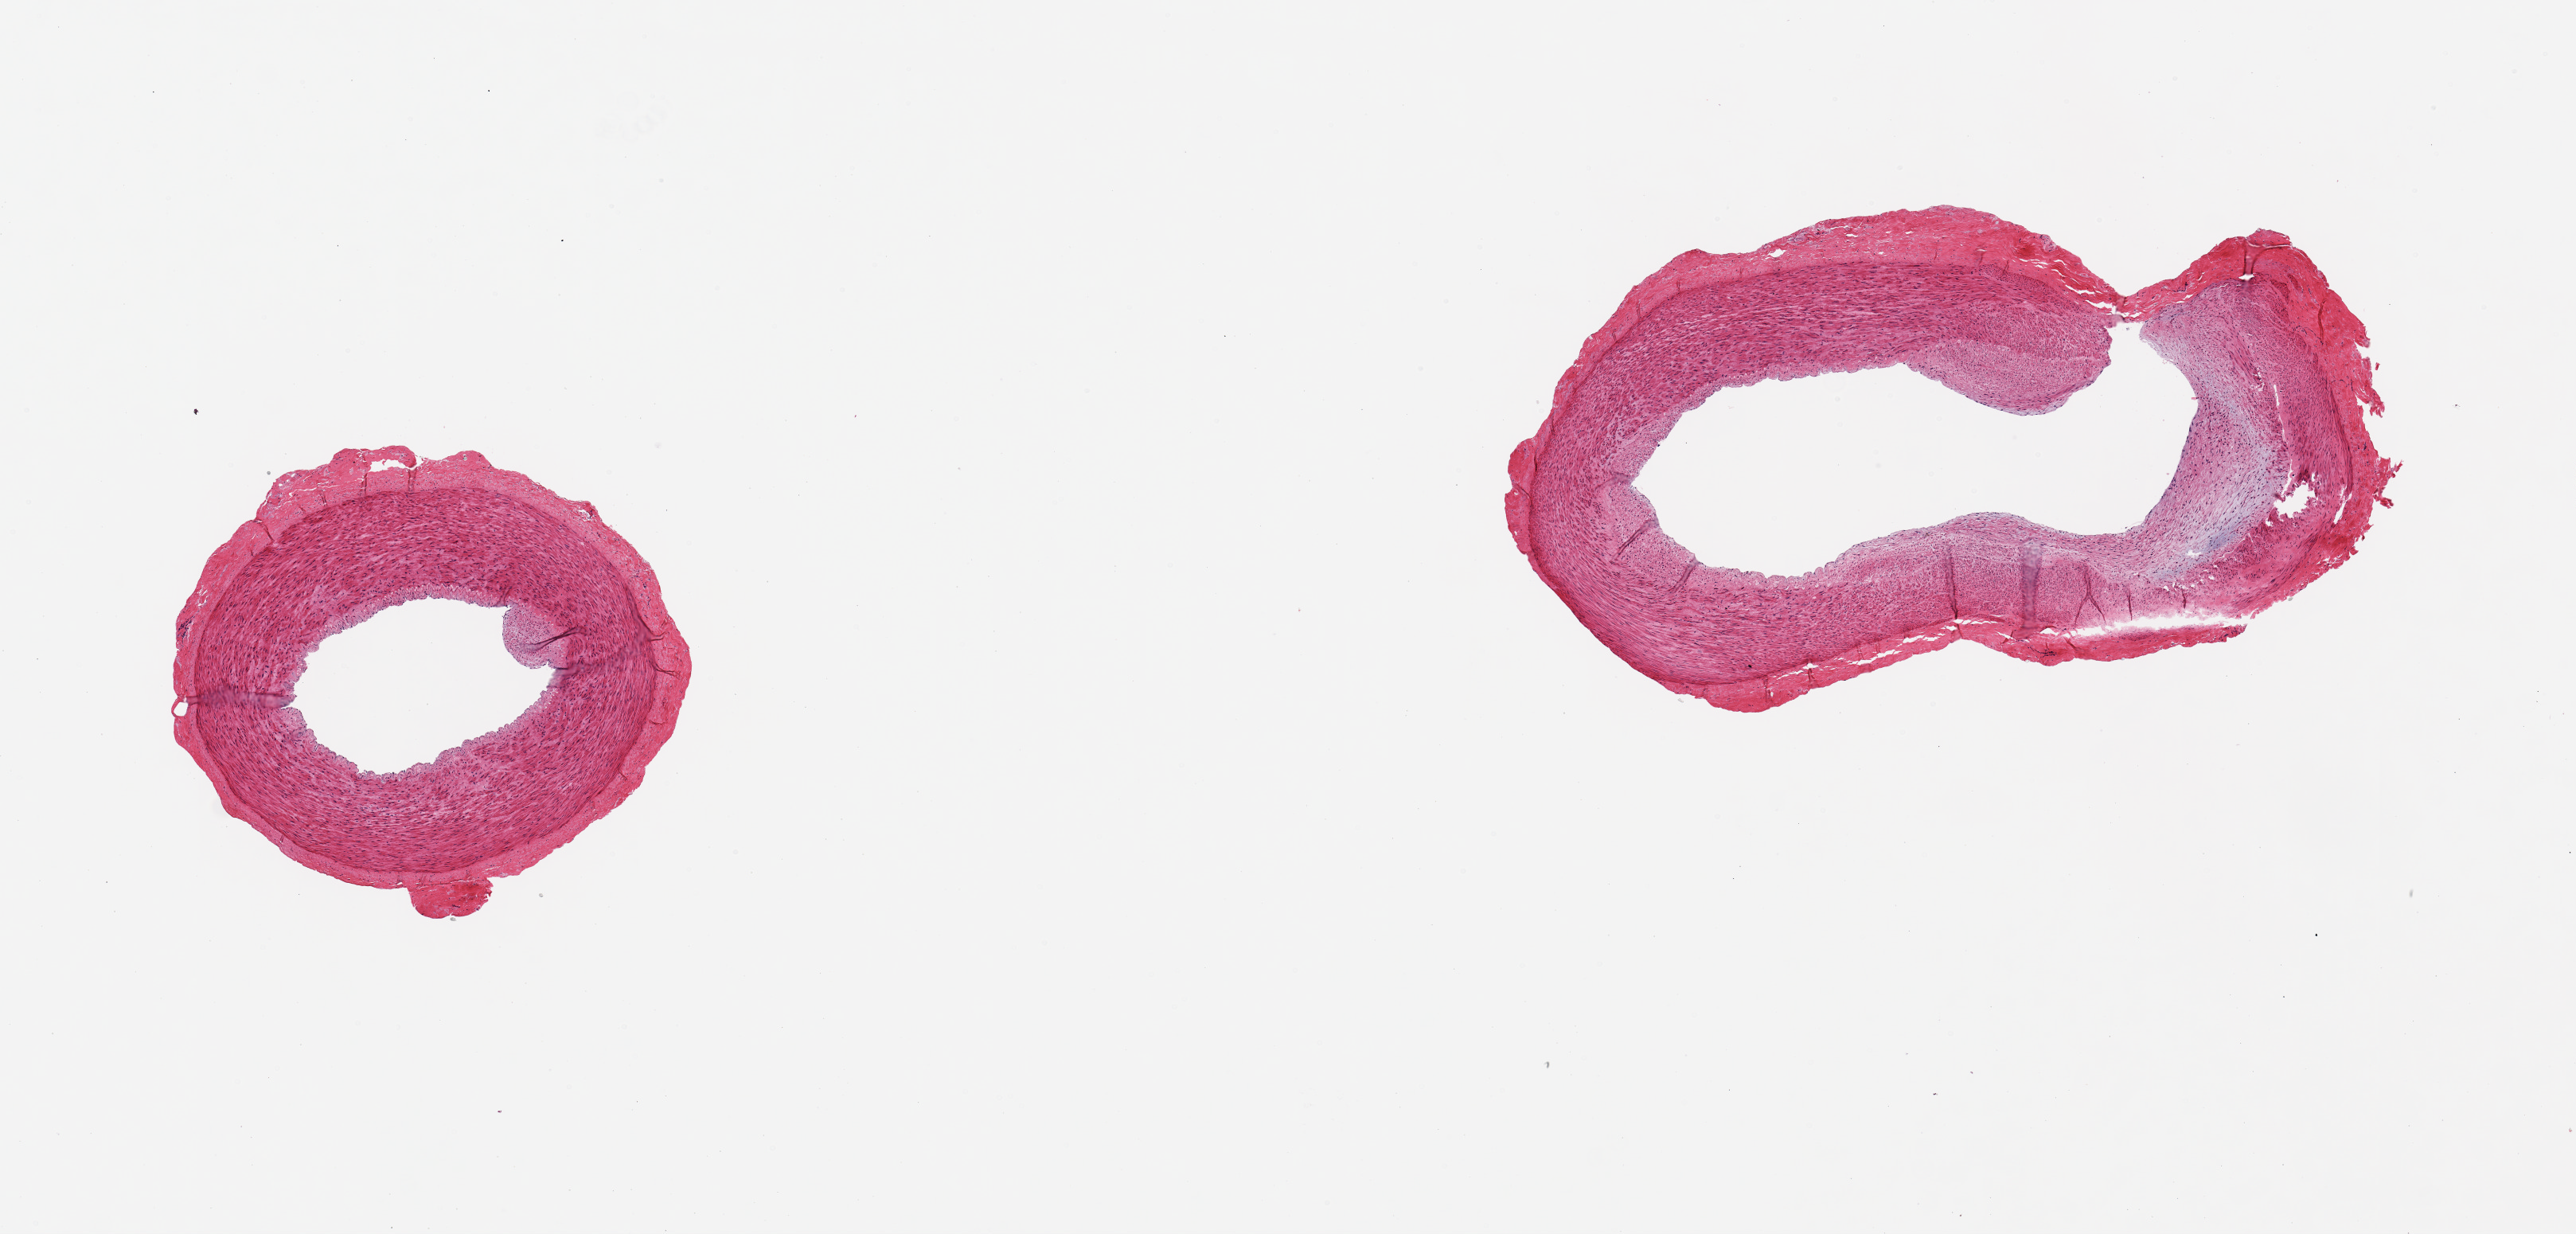
Hematoxylin and eosin (H&E) whole-slide image, shown as a low-resolution overview of the whole scanned area (about 12.8 x 6.1 mm, slide scanned at 20x), PAXgene-fixed paraffin-embedded (PFPE) section, target tissue: tibial artery, donor tissue sample. Donor: male.
Reviewer comment on this tissue sample: 2 pieces, 2.5x2 & 4x2mm; small plaques.